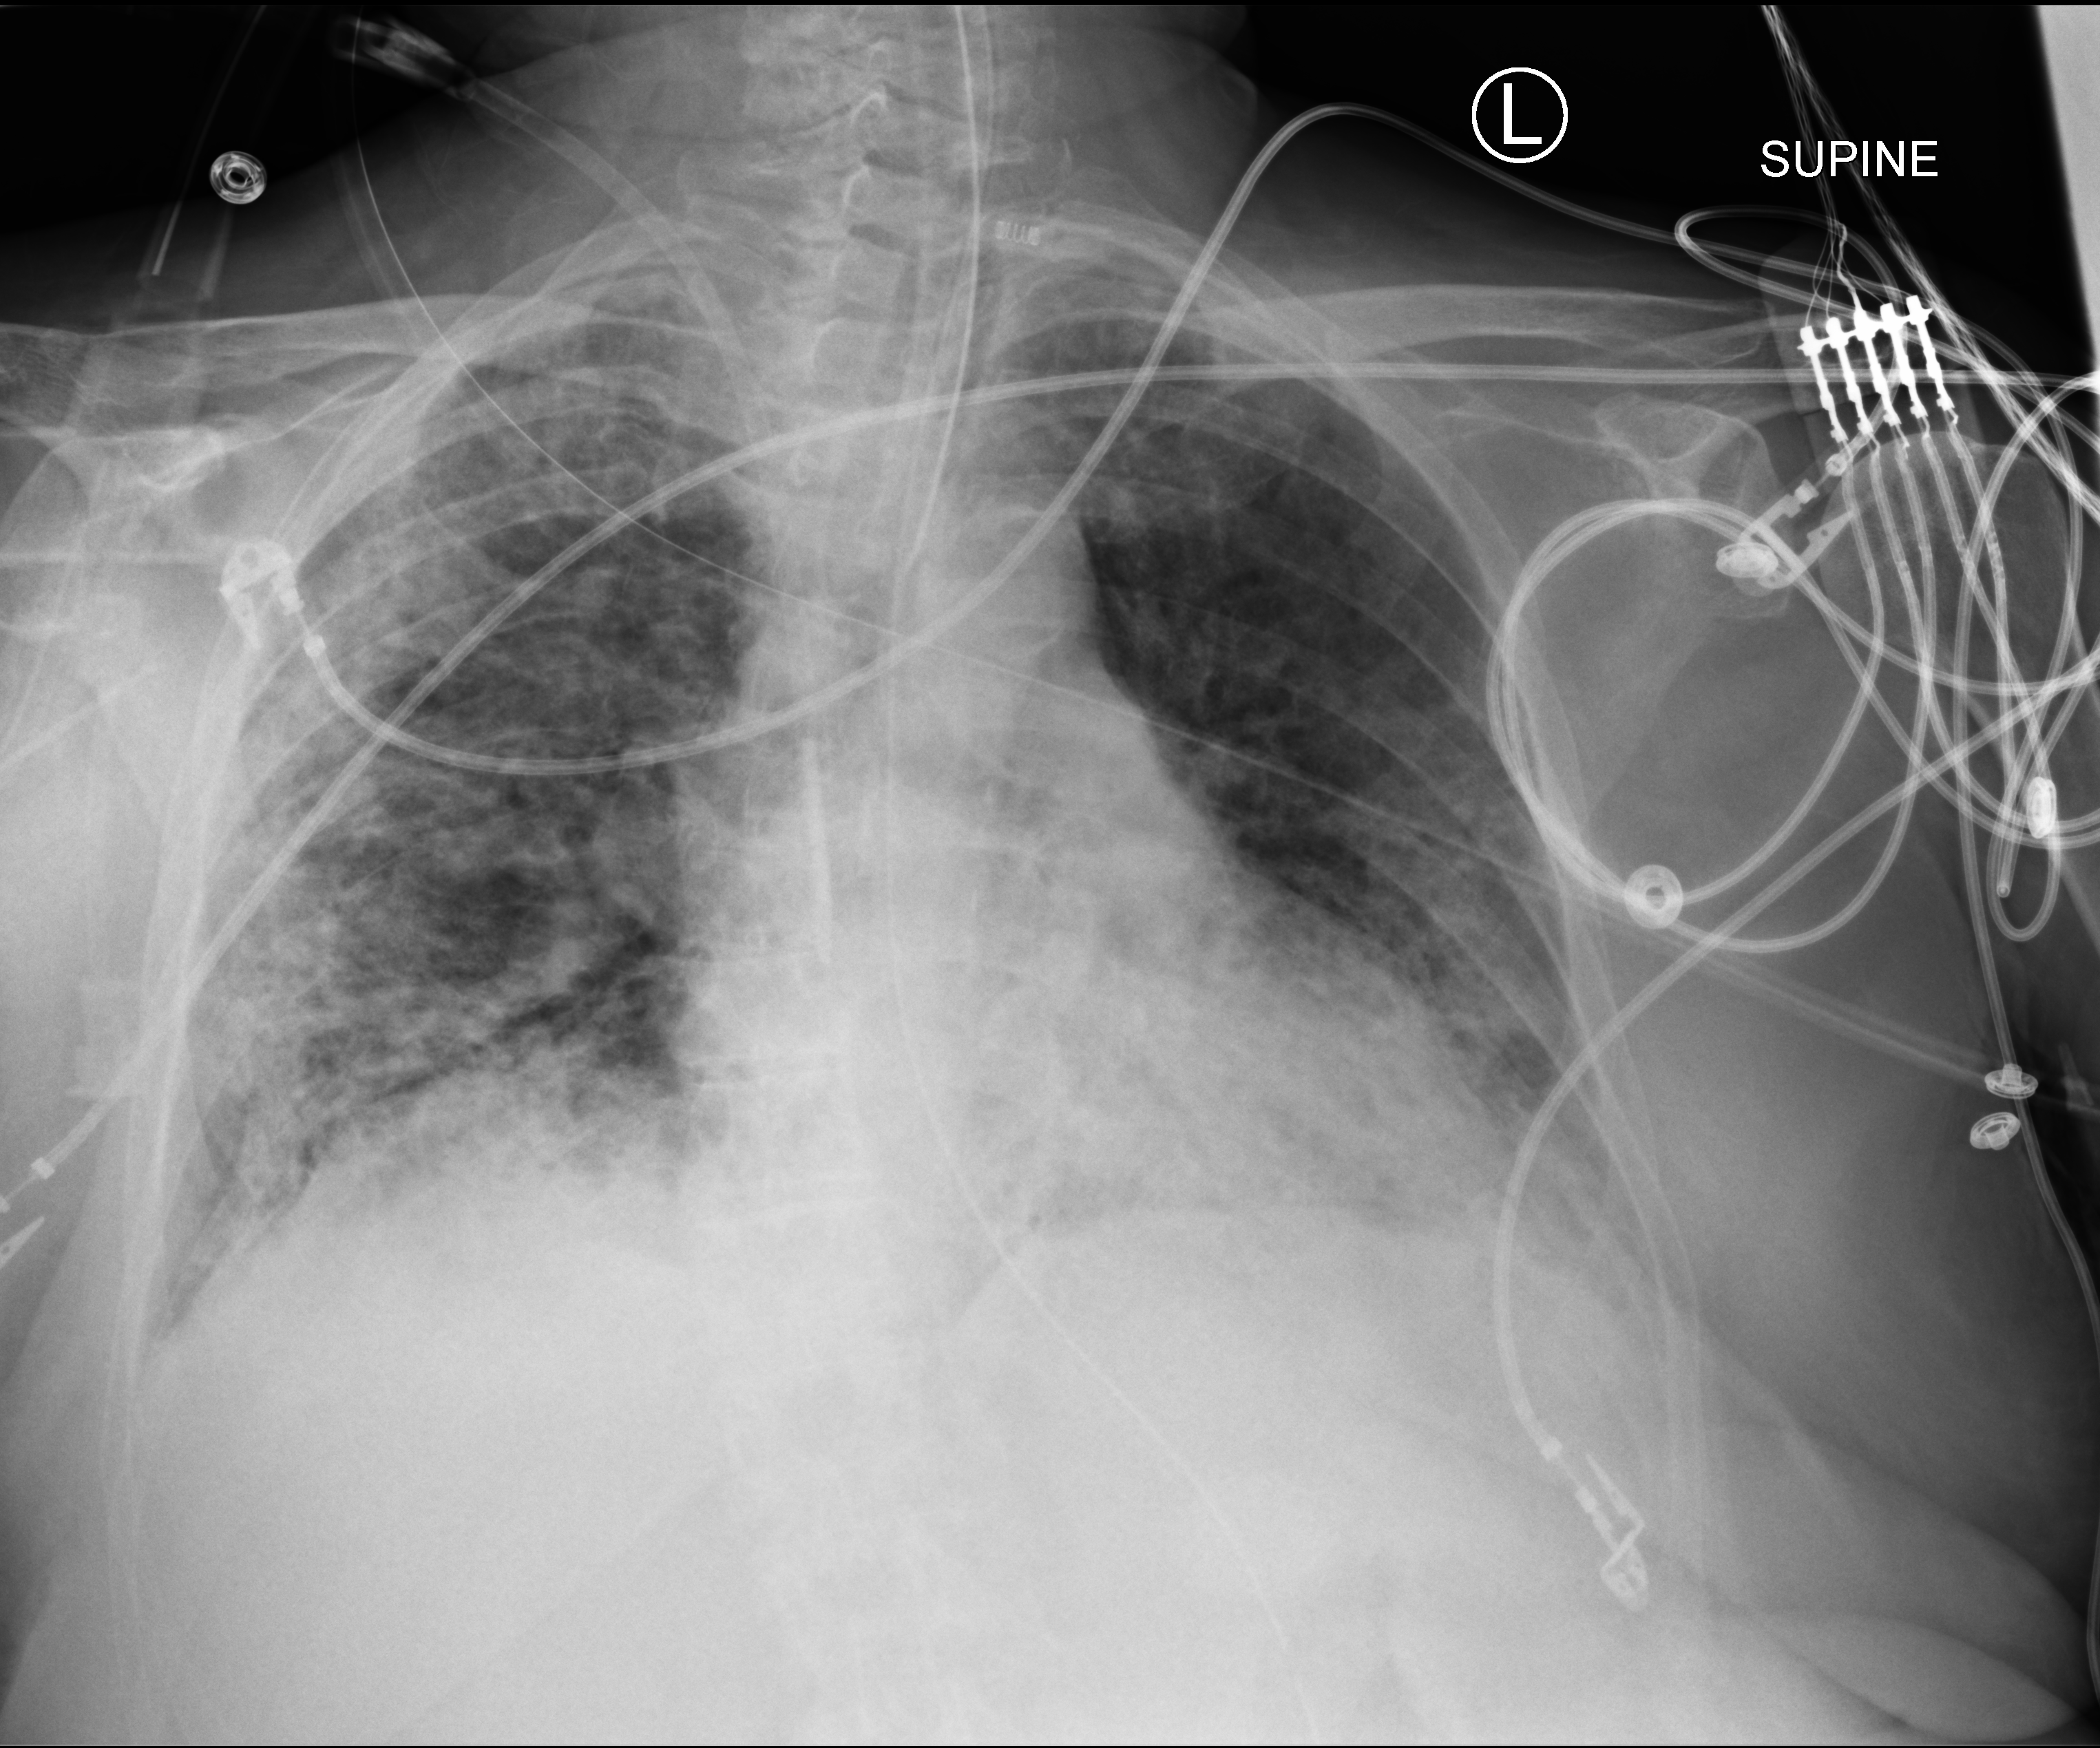
Portable chest radiograph; anteroposterior (AP) projection. Patient hospitalised with COVID-19; female, aged 75–90 years.
Hospital-stay facts (about this admission, not read from this image; timing relative to this image not recorded):
- admitted to intensive care during this hospital stay: yes